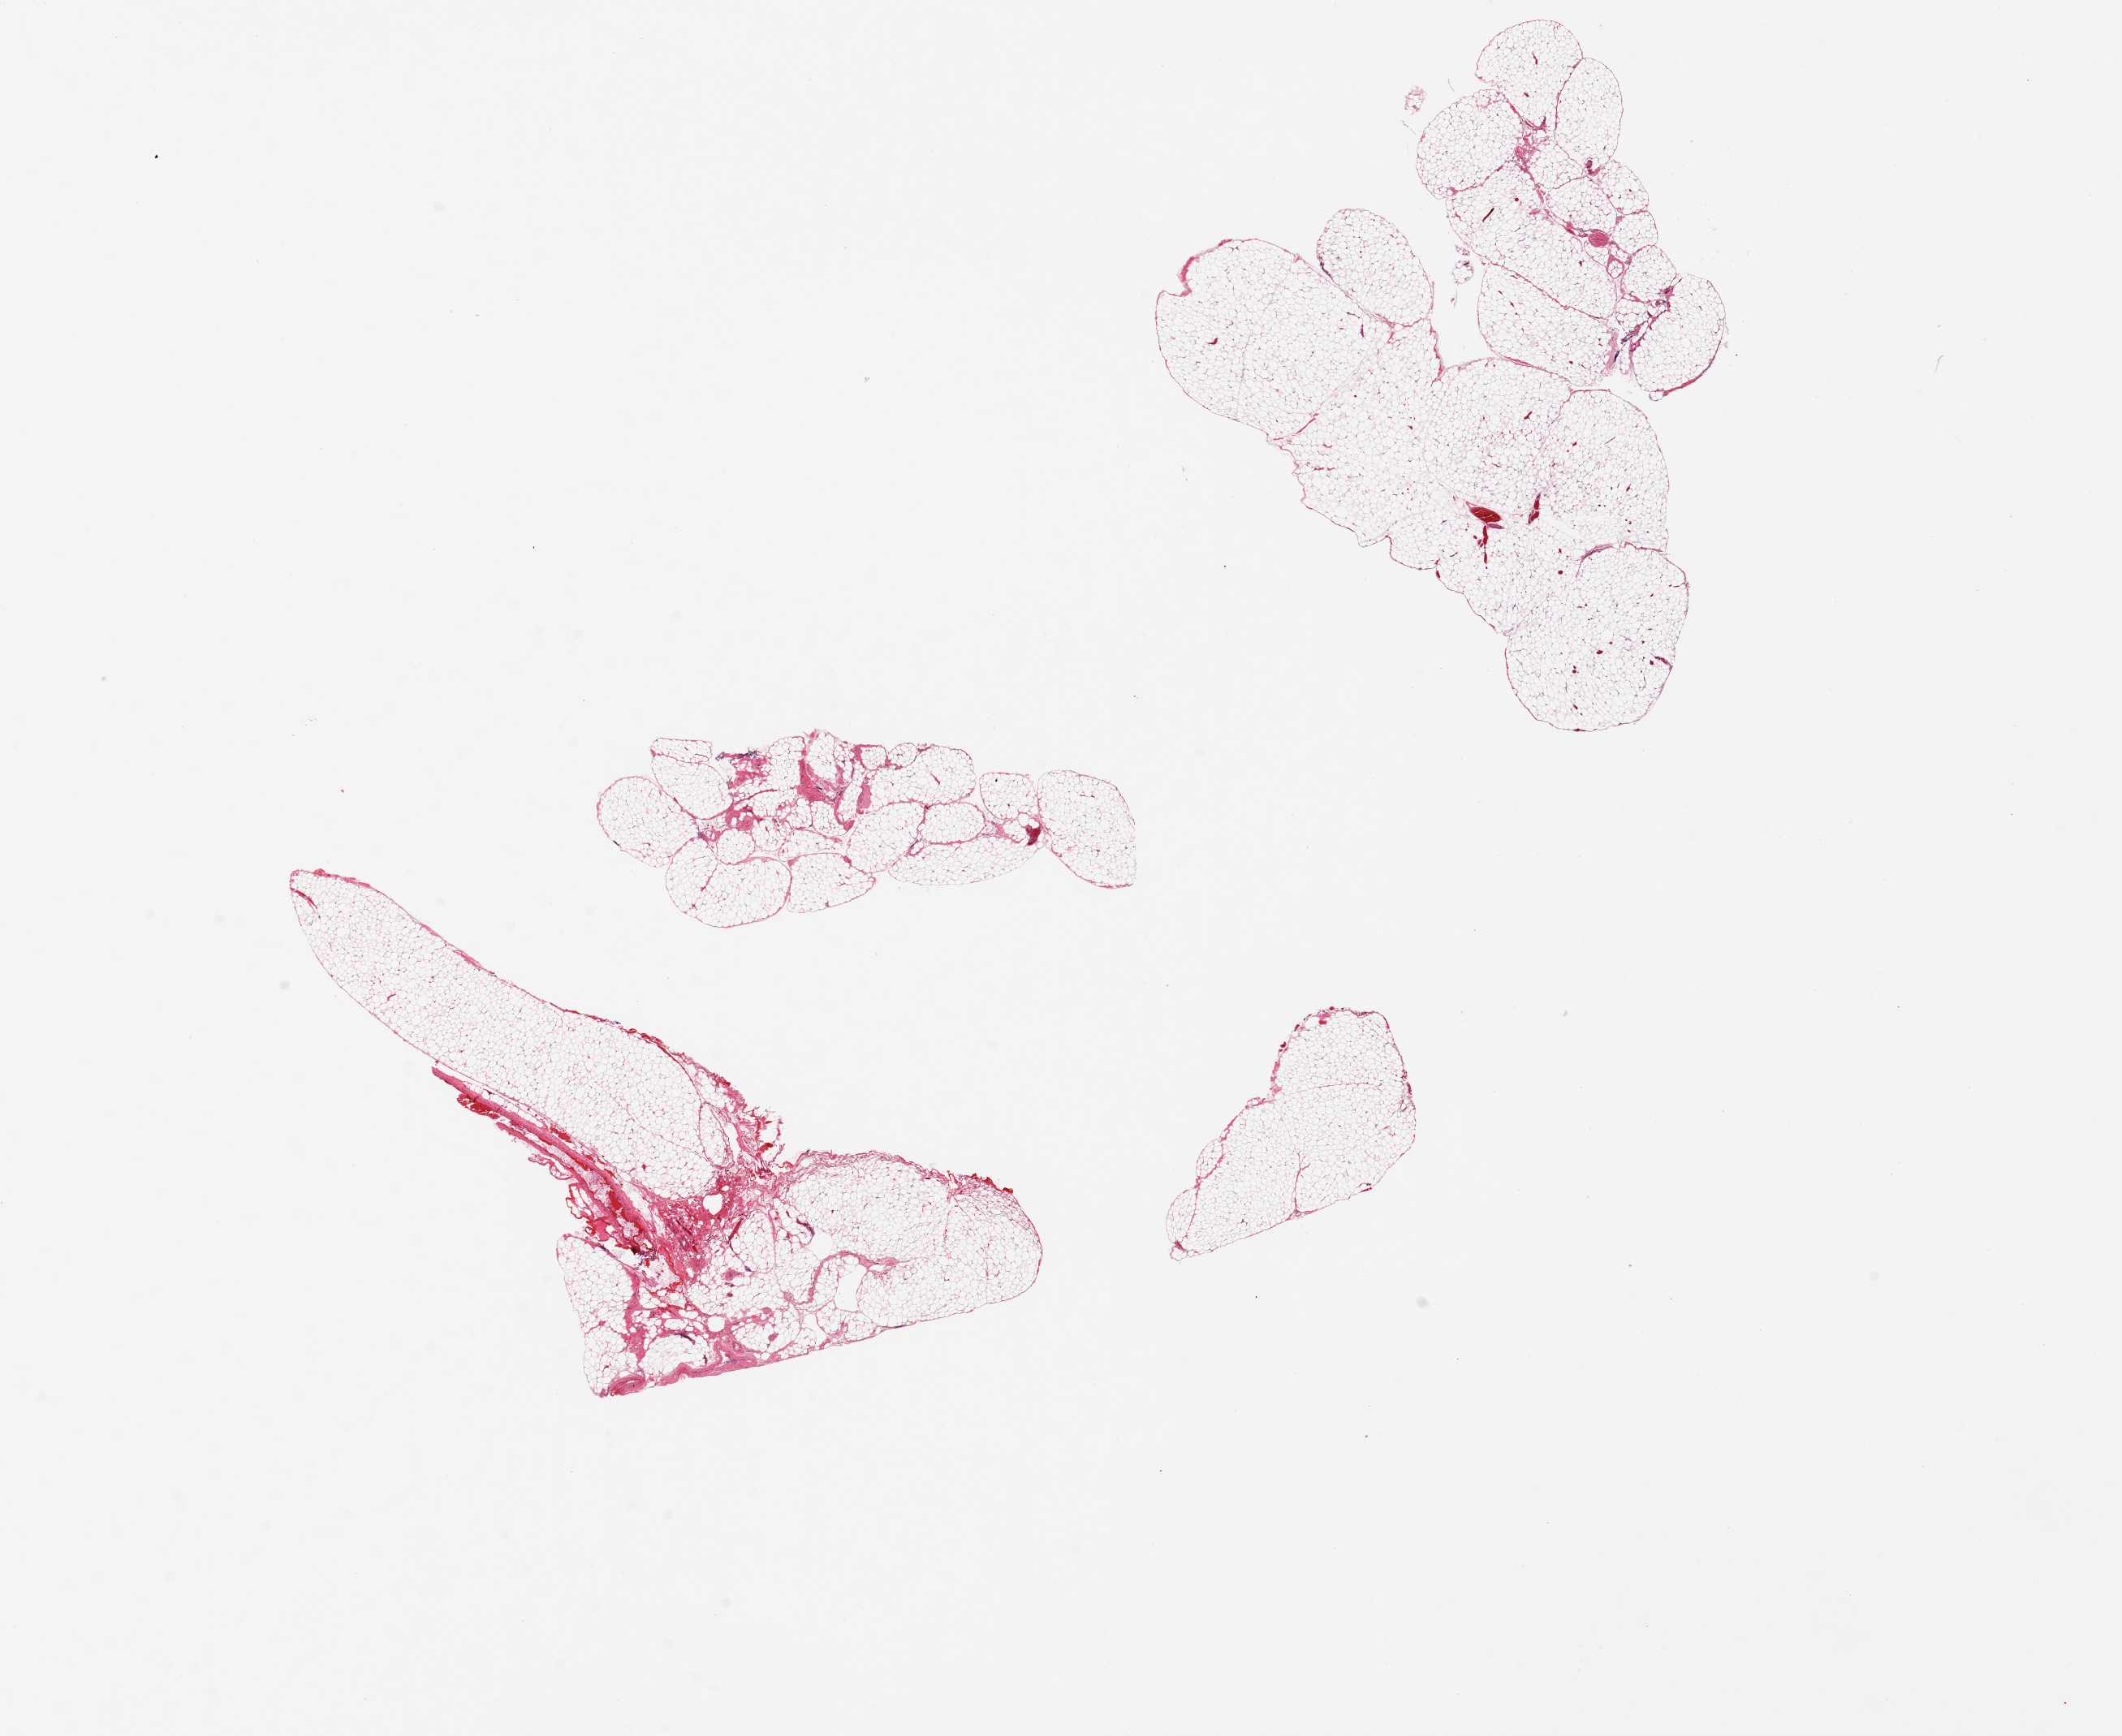
Whole-slide image, H&E stain, brightfield, shown as a low-resolution overview of the whole scanned area (about 20.7 x 16.9 mm, from a 20x scan), PAXgene-fixed paraffin-embedded (PFPE) section, target tissue: omentum, tissue donor sample. Donor: male.
Review note (as recorded): 2 pieces, ~10 fiborvacular tissue.